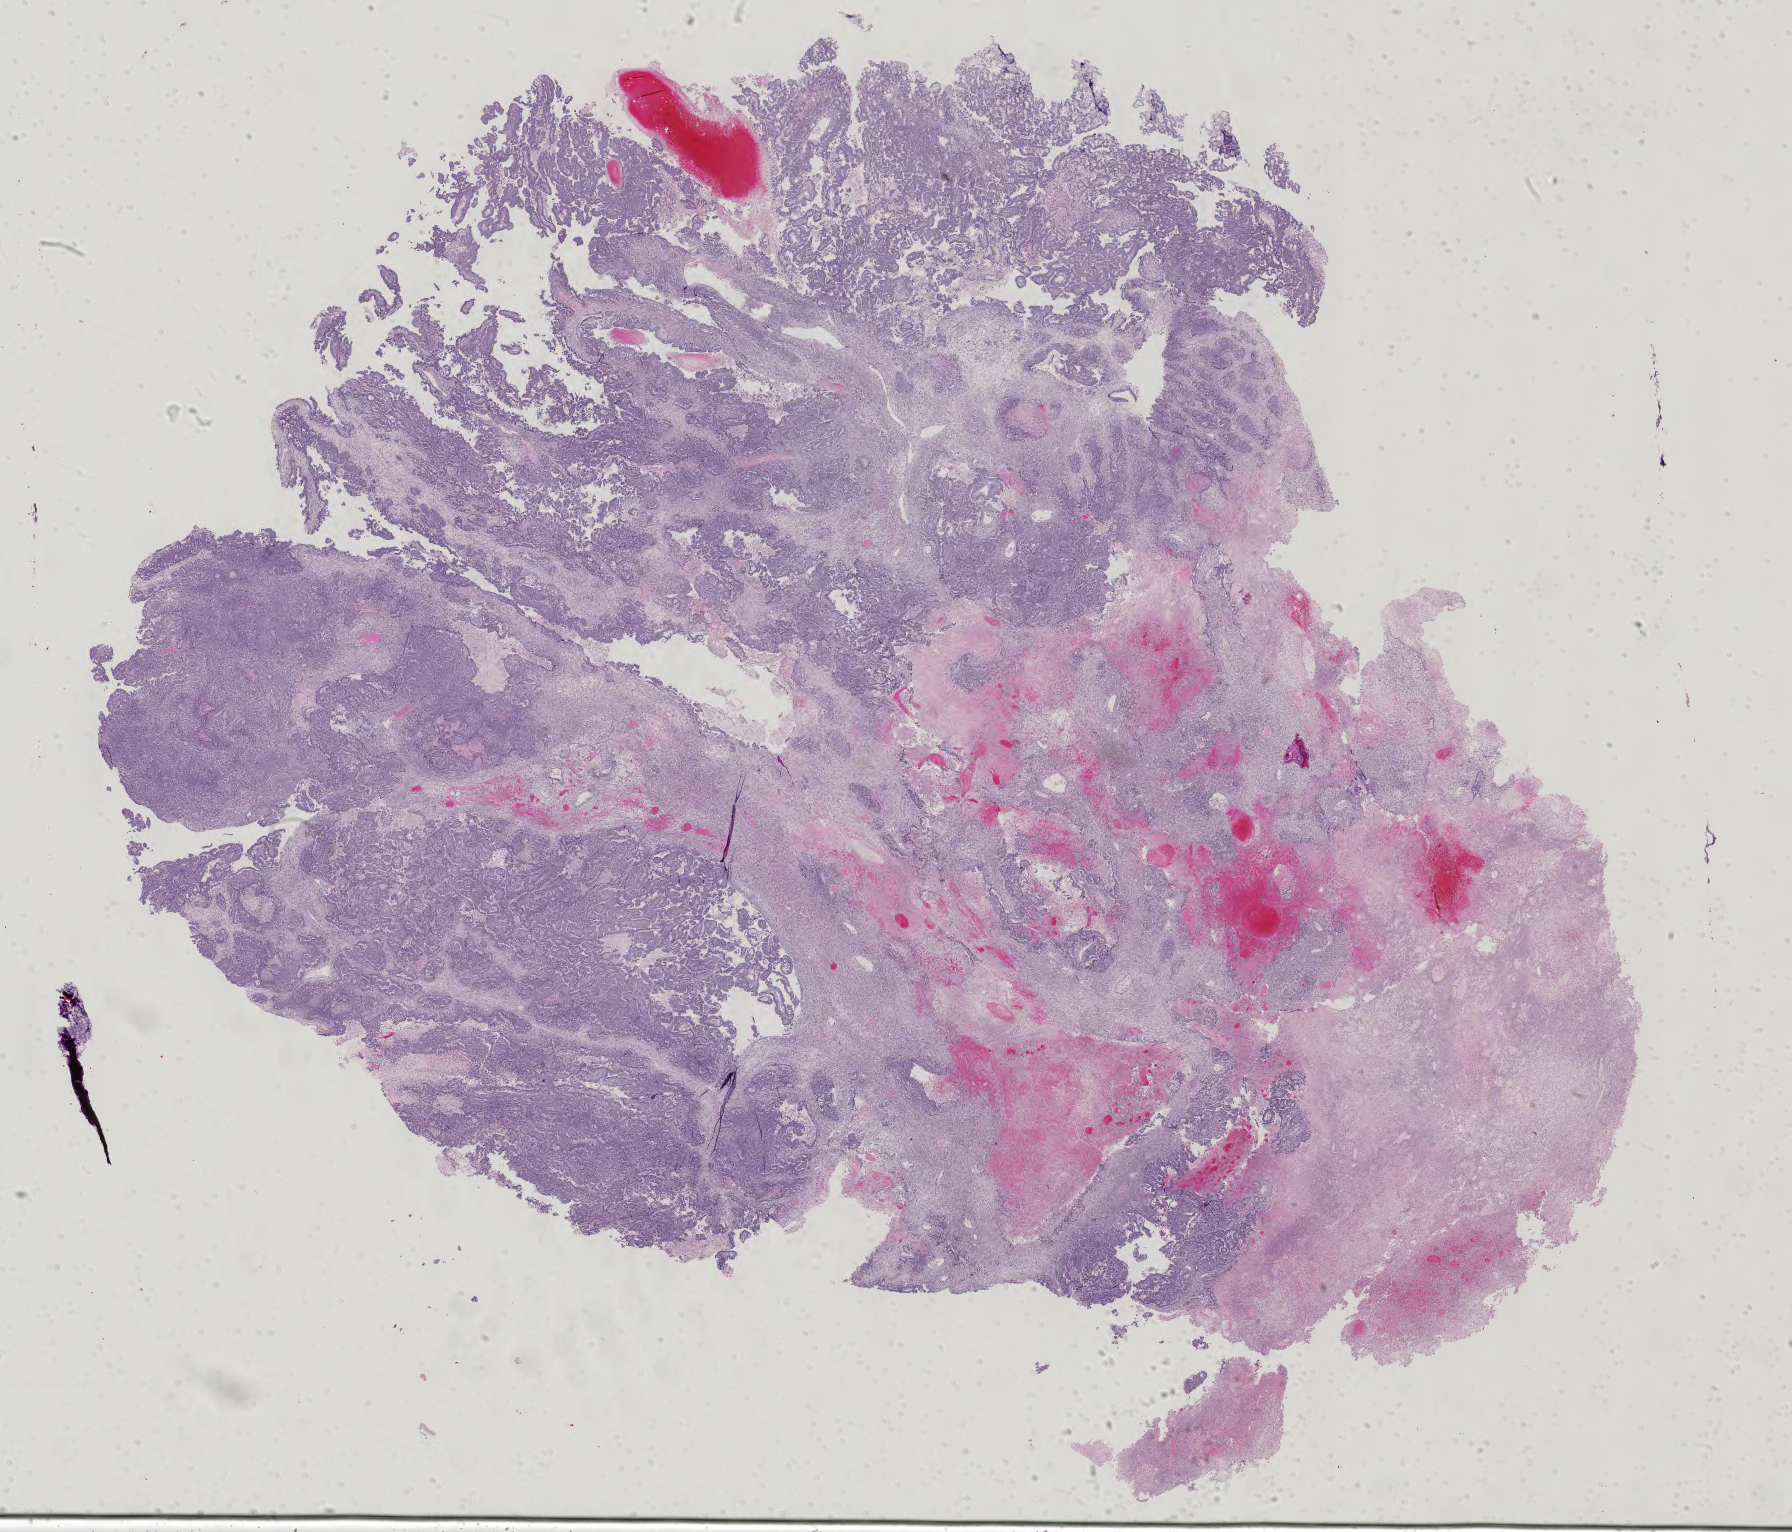
Digitized H&E tissue section (whole slide), low-resolution overview of the scanned area, about 26.1 x 22.3 mm (from a 40x scan), FFPE section, testis, primary tumour sample. Patient: male, age at initial diagnosis 26 years.
AJCC pathologic stage: IIIB (7th edition). Diagnosis: Embryonal carcinoma, NOS.